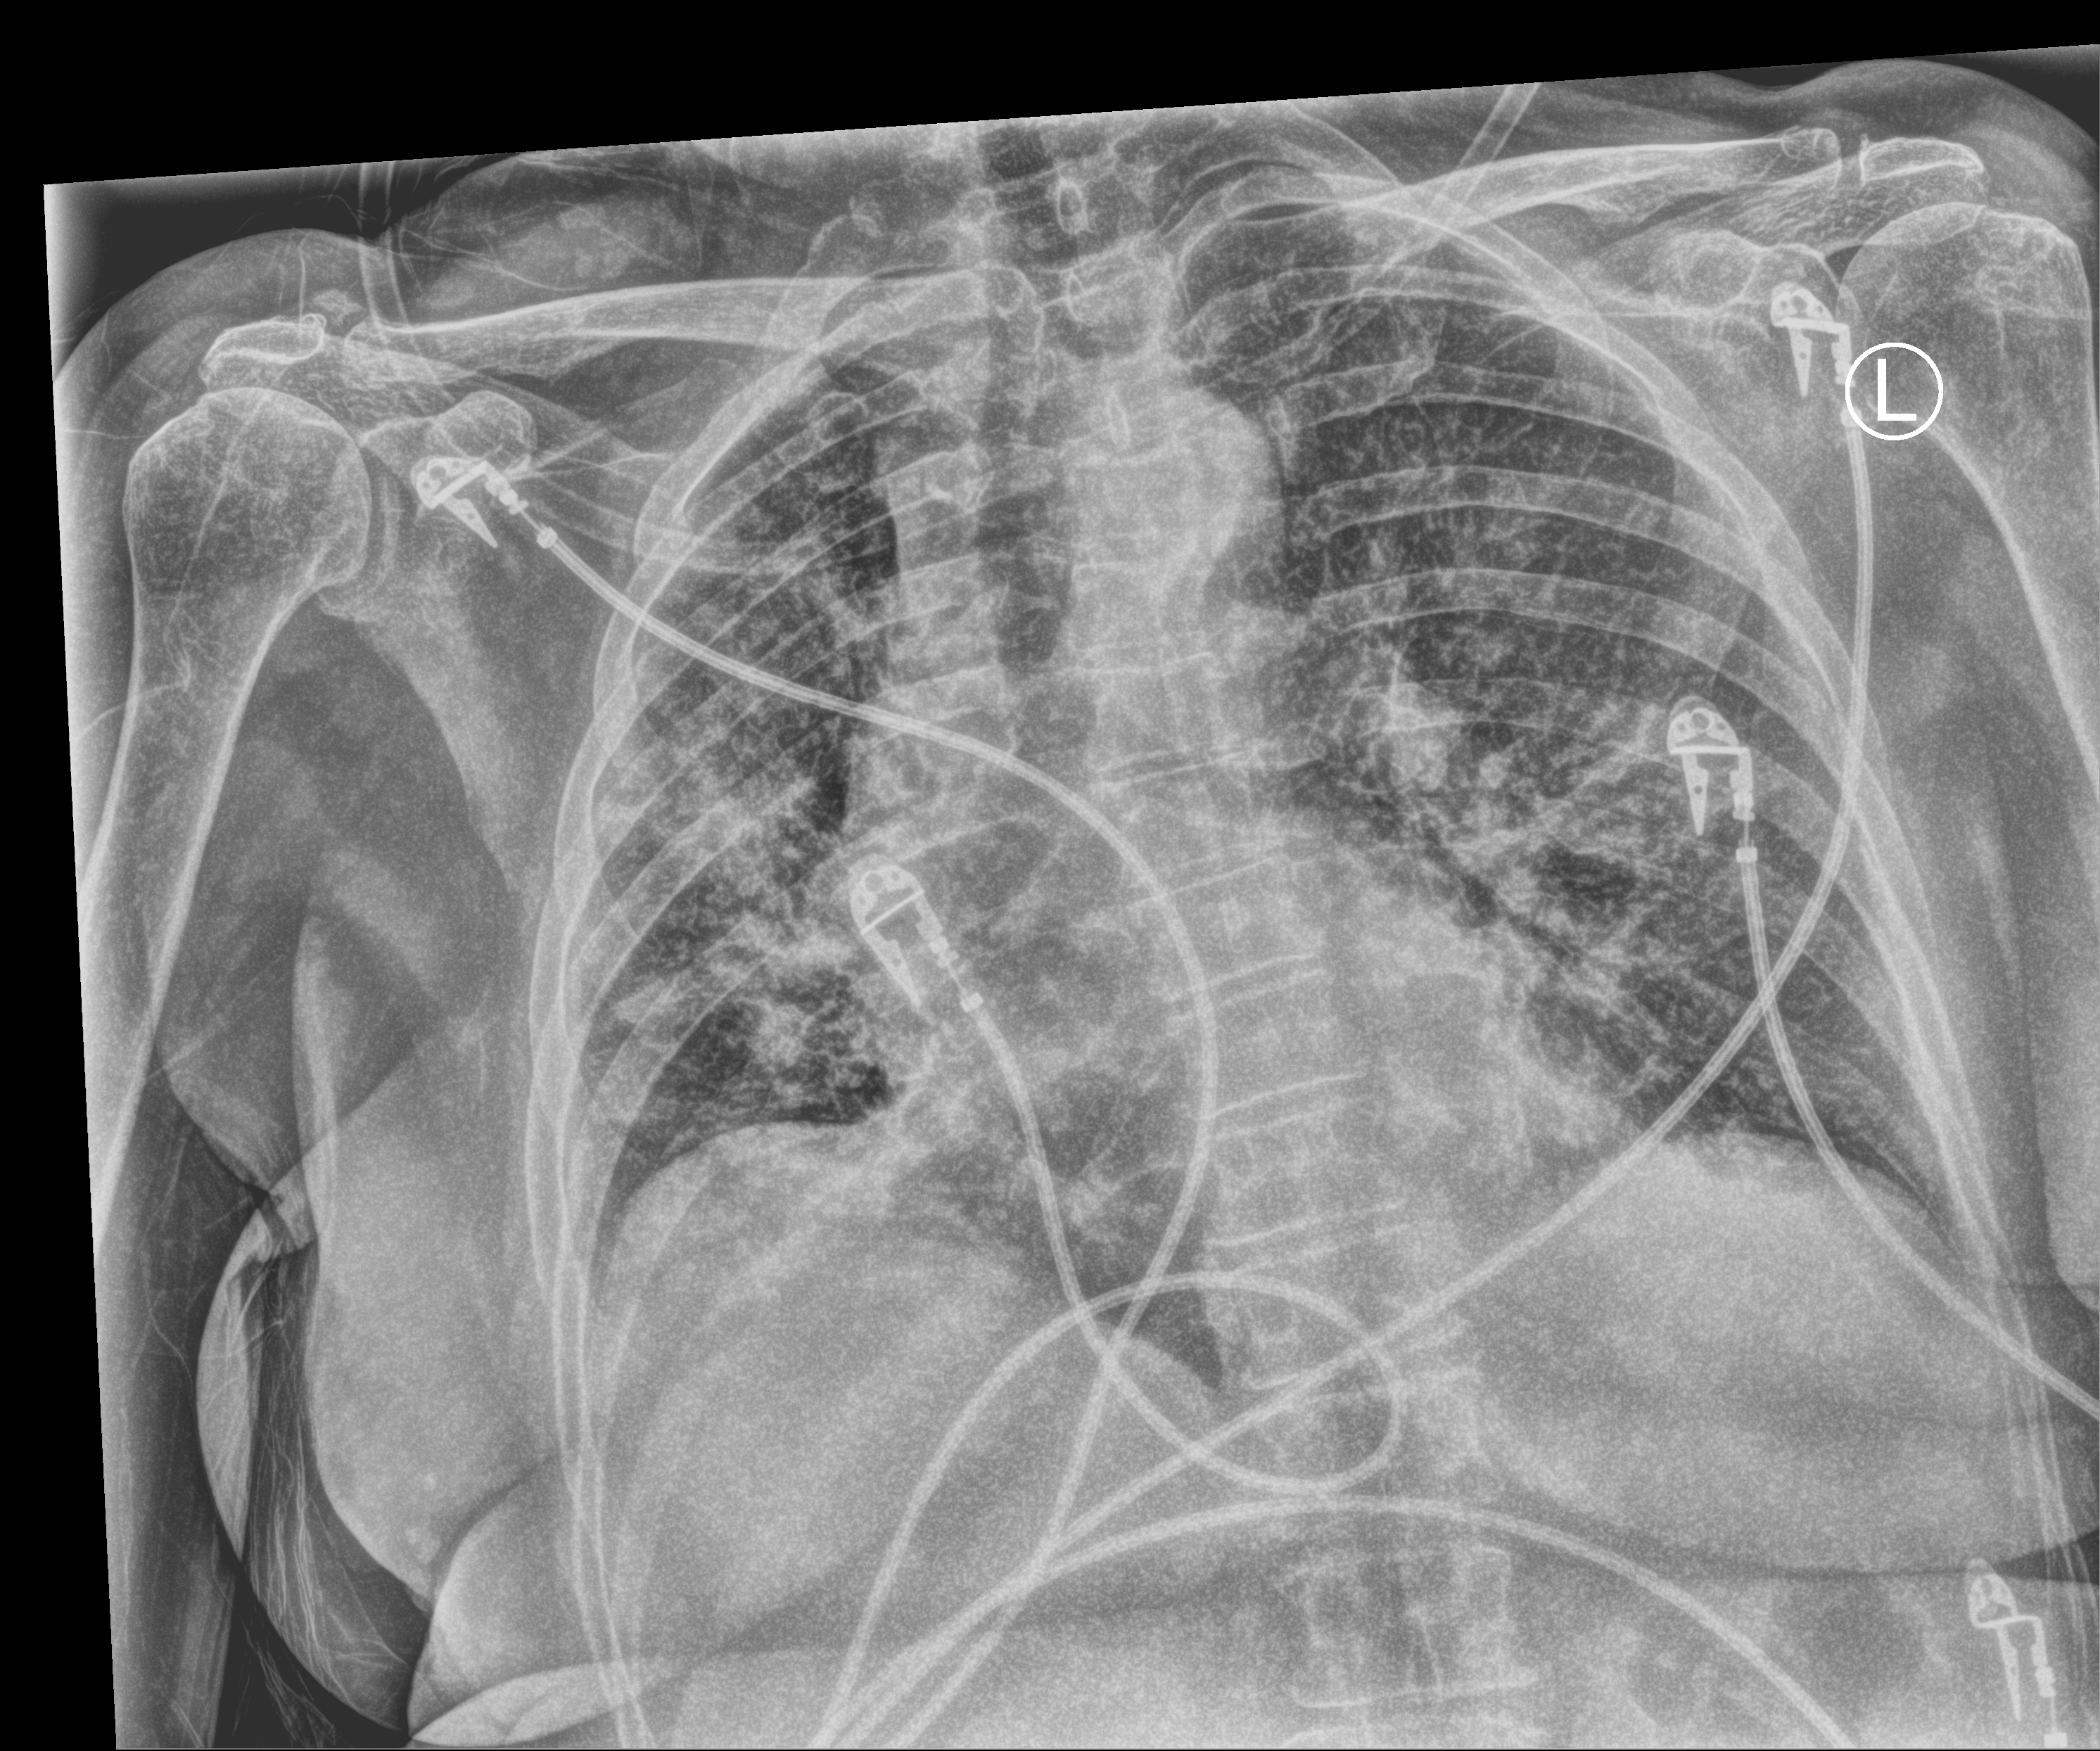
Chest X-ray (portable), anteroposterior (AP) projection. Female patient hospitalised with COVID-19, age 75–90 years.
Admission-level facts for this patient (not findings on this image; timing relative to this image not recorded):
- mechanically ventilated during this hospital stay: no
- length of hospital stay: 4 days